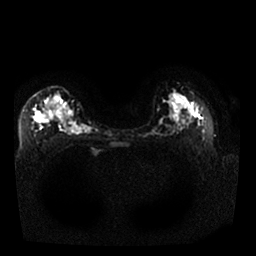
Breast MRI, one axial slice; slice 16 of 25 in the series (ordered by position); diffusion-weighted series; image 2 of 4 stored at this slice position (different b-values; order by instance number); 1.5 T; 4 mm slice thickness; 256 × 256 image matrix. Female patient.
Annotated regions visible in this slice (expert manual segmentation):
- tumour on diffusion-weighted imaging: bounding box <42,105,66,121> (left, top, right, bottom; pixels)